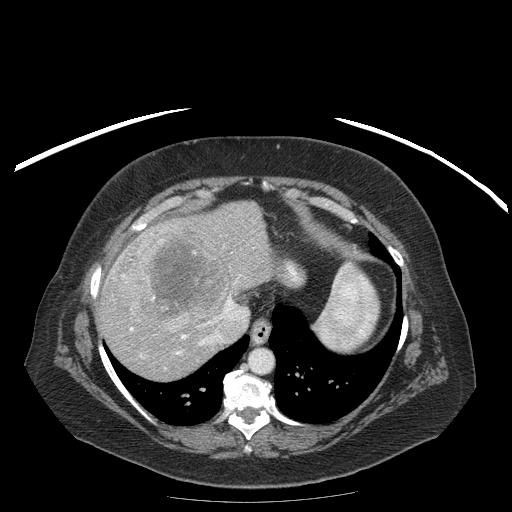
Contrast-enhanced abdominal CT (liver protocol), one axial slice. Position 151 of 204 along the scan axis. Reconstruction kernel STANDARD. 120 kVp. Soft-tissue window (W 400 / L 40 HU). 512 × 512 image matrix. From the clinical record (not read from this slice): diagnosis: hepatocellular carcinoma (patient treated with transarterial chemoembolisation; whether this scan precedes or follows treatment is not stated here); TNM stage (as recorded): Stage-IIIB; Child-Pugh class: A; tumour nodularity: uninodular.
Outlined on this slice (semi-automatically segmented with operator editing):
- liver parenchyma outside the tumour (the mass and vessels are separate outlines, so this box may not span the whole liver): bounding box [x1, y1, x2, y2] px = [96, 202, 282, 380]
- mass: [119, 232, 229, 333]
- liver vessels: [113, 233, 247, 358]